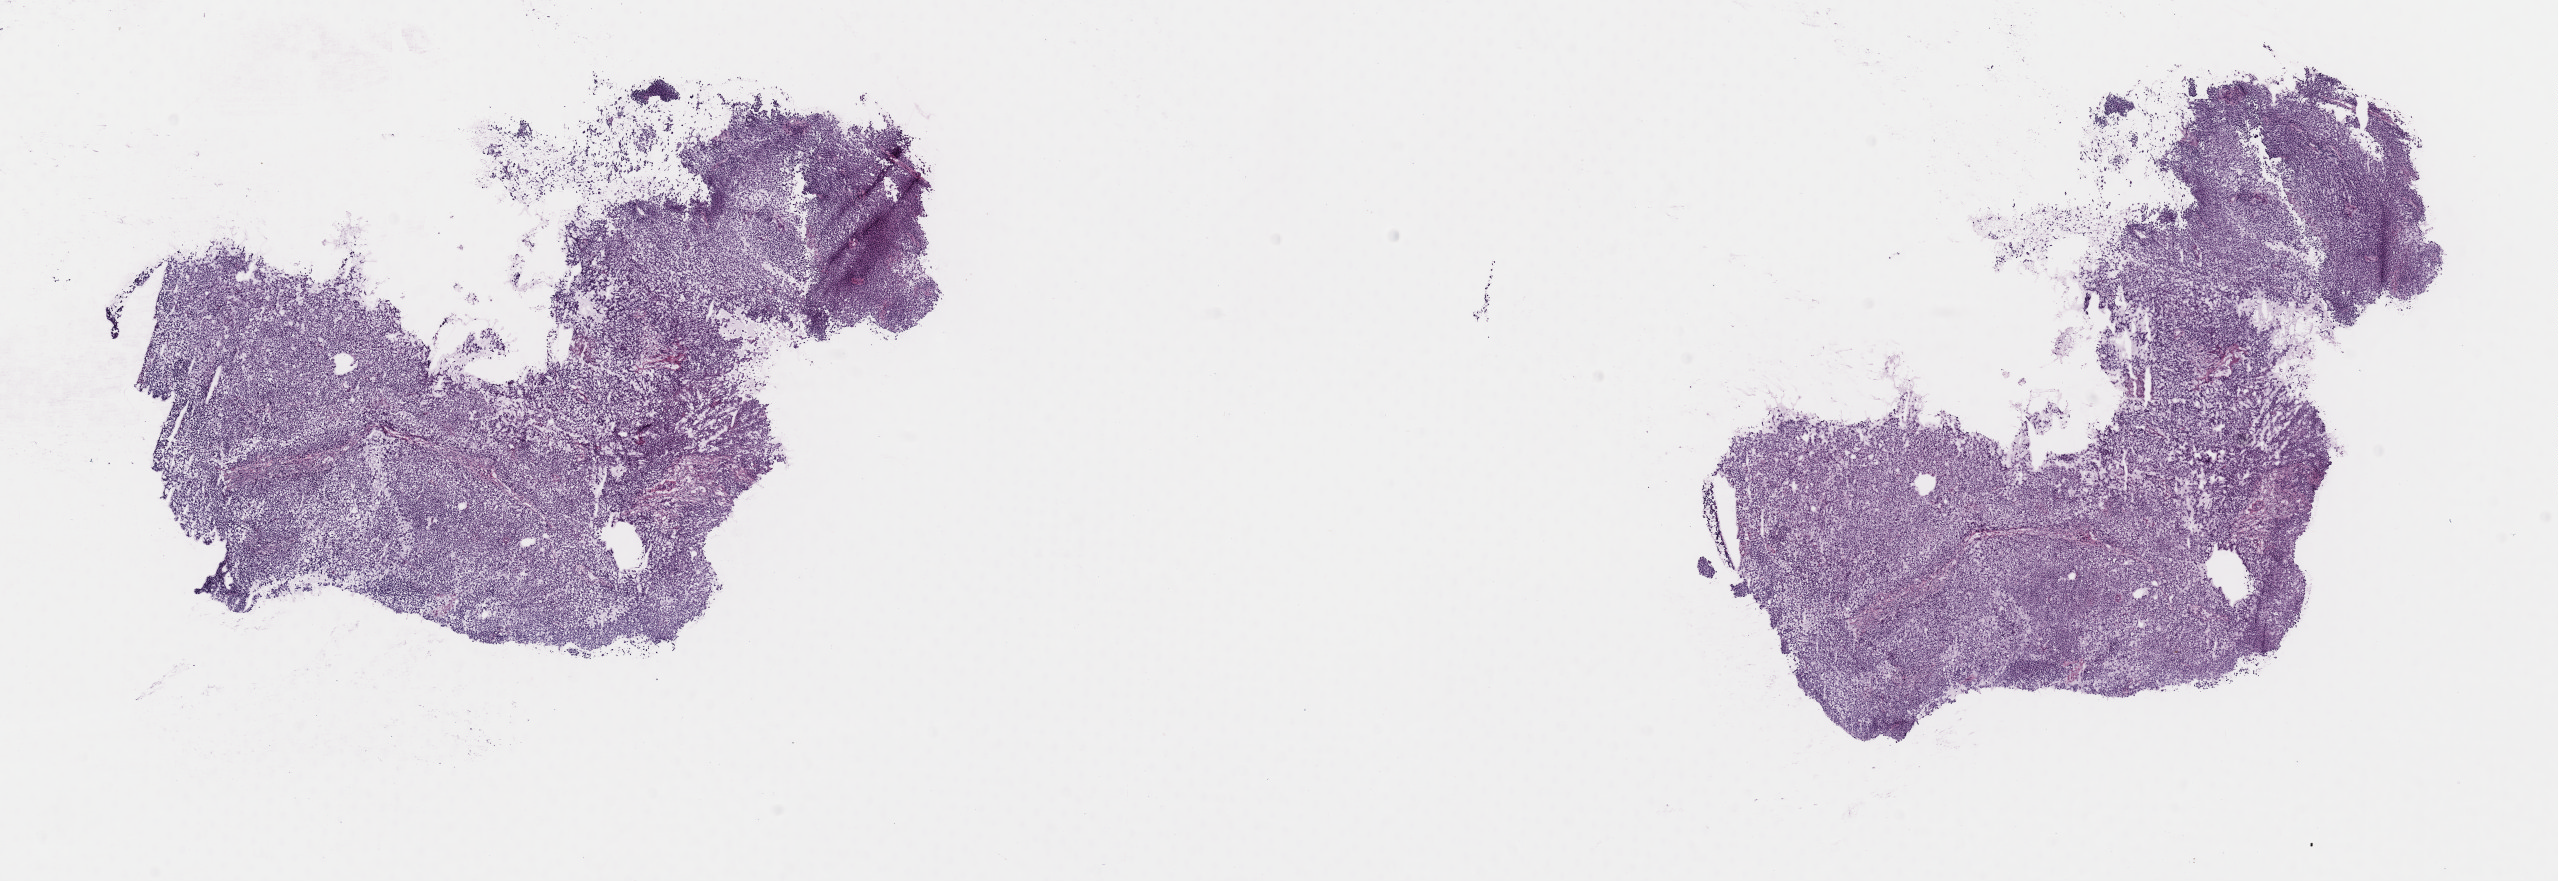
H&E-stained whole-slide image, a low-resolution overview of the entire scanned area, about 20.2 x 7.0 mm (slide scanned at 40x), frozen section from the top of the tissue portion, metastatic tumour sample, sampled site: lymph nodes of axilla or arm. Female, age 40 years at initial diagnosis. Slide review estimates, as recorded: tumour cells 100%, tumour nuclei 96%, normal cells 0%, stromal cells 0%, necrosis 0%. Infiltration values recorded for this section: lymphocyte infiltration 0%, monocyte infiltration 0%, neutrophil infiltration 0%.
This section: metastatic tumour tissue. Patient diagnosis: Malignant melanoma, NOS.